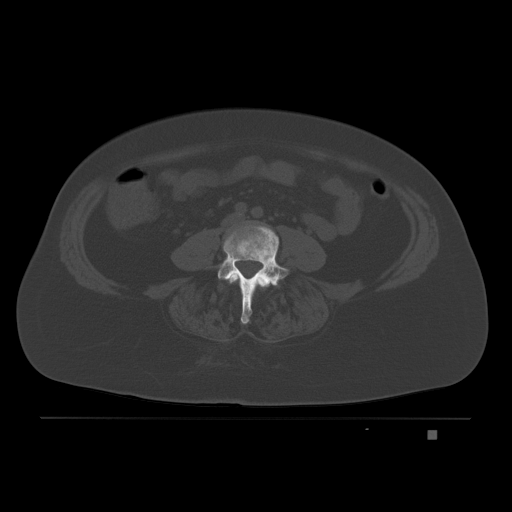
CT including the spine, one axial slice. Slice 42 of 221 in the series (ordered by position). Bone window (W 1800 / L 400 HU). 3 mm slice thickness. 512 × 512 image matrix, field of view 474 × 474 mm. Patient: female, 63 years. From the clinical record (not read from this slice): primary cancer: breast.
Annotated regions visible in this slice (semi-automatic segmentation, software-assisted and operator-edited):
- L3 vertebra: bounding box <229,274,269,288> (left, top, right, bottom; pixels)
- L4 vertebra: <208,225,290,324>